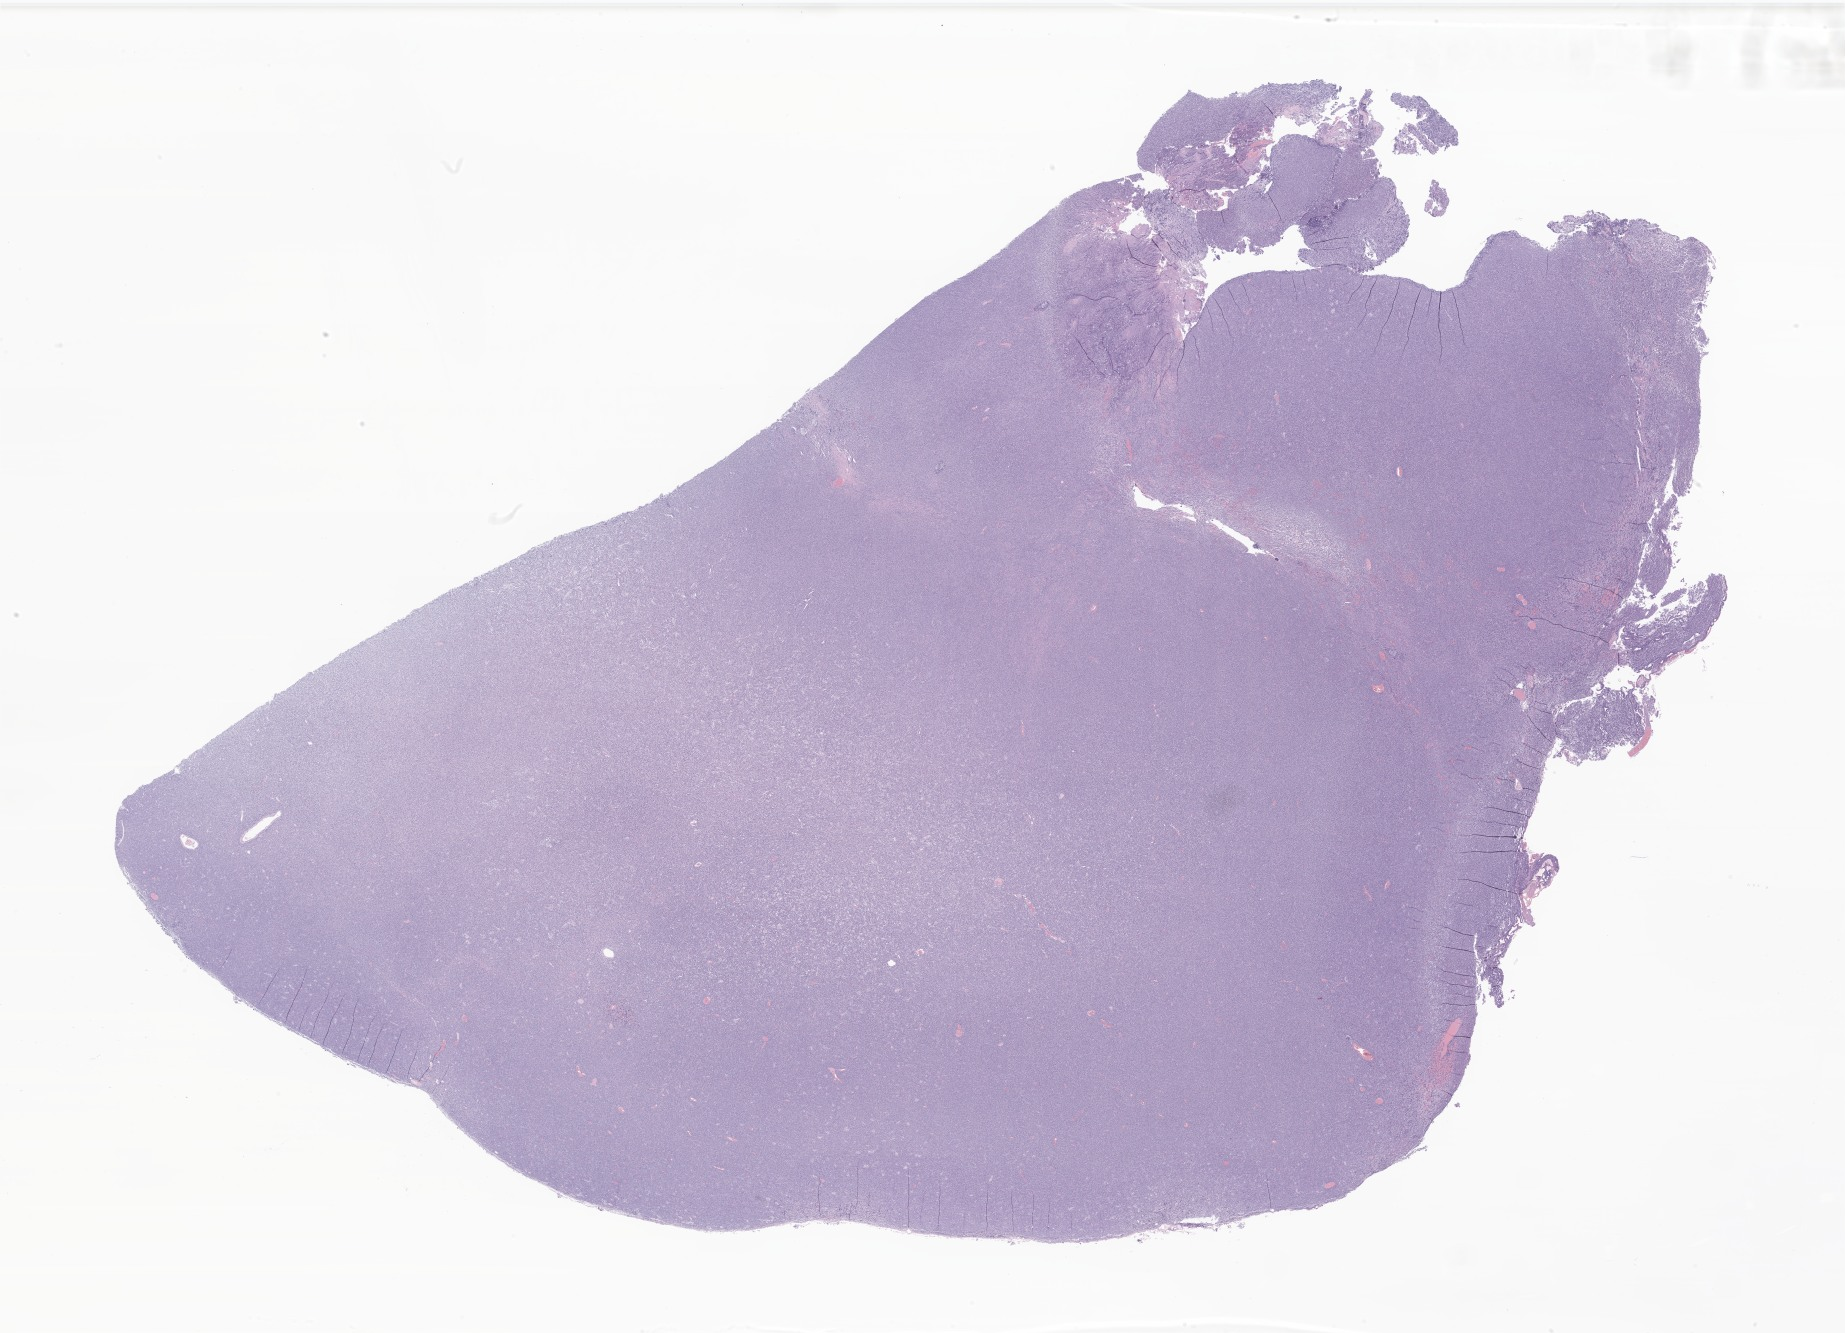
Haematoxylin and eosin whole-slide image of tumor tissue from the cerebellum — whole scanned area (about 31.1 x 22.5 mm) shown as a low-resolution overview, formalin-fixed, paraffin-embedded (FFPE) tissue. Patient female; age 247 months (20 years 7 months).
Diagnosis (ICD-O-3 morphology term): Medulloblastoma, NOS.